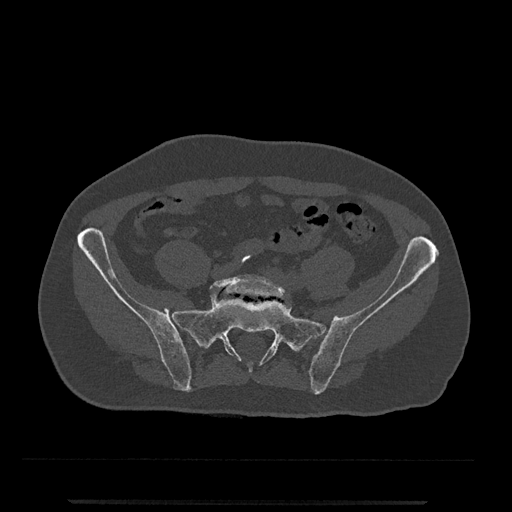
CT including the spine, one axial slice. Position 24 of 797 along the scan axis. Reconstruction kernel Br40s/3. Bone window (W 1800 / L 400 HU). 0.5 mm slice thickness. 512 × 512 image matrix, field of view 419 × 419 mm. Male patient, age 63 years. Case-level facts recorded for this patient, not image findings: primary cancer: prostate.
Structures marked on this image (semi-automatically segmented with operator editing):
- L5 vertebra: bounding box [x1, y1, x2, y2] px = [210, 275, 291, 299]